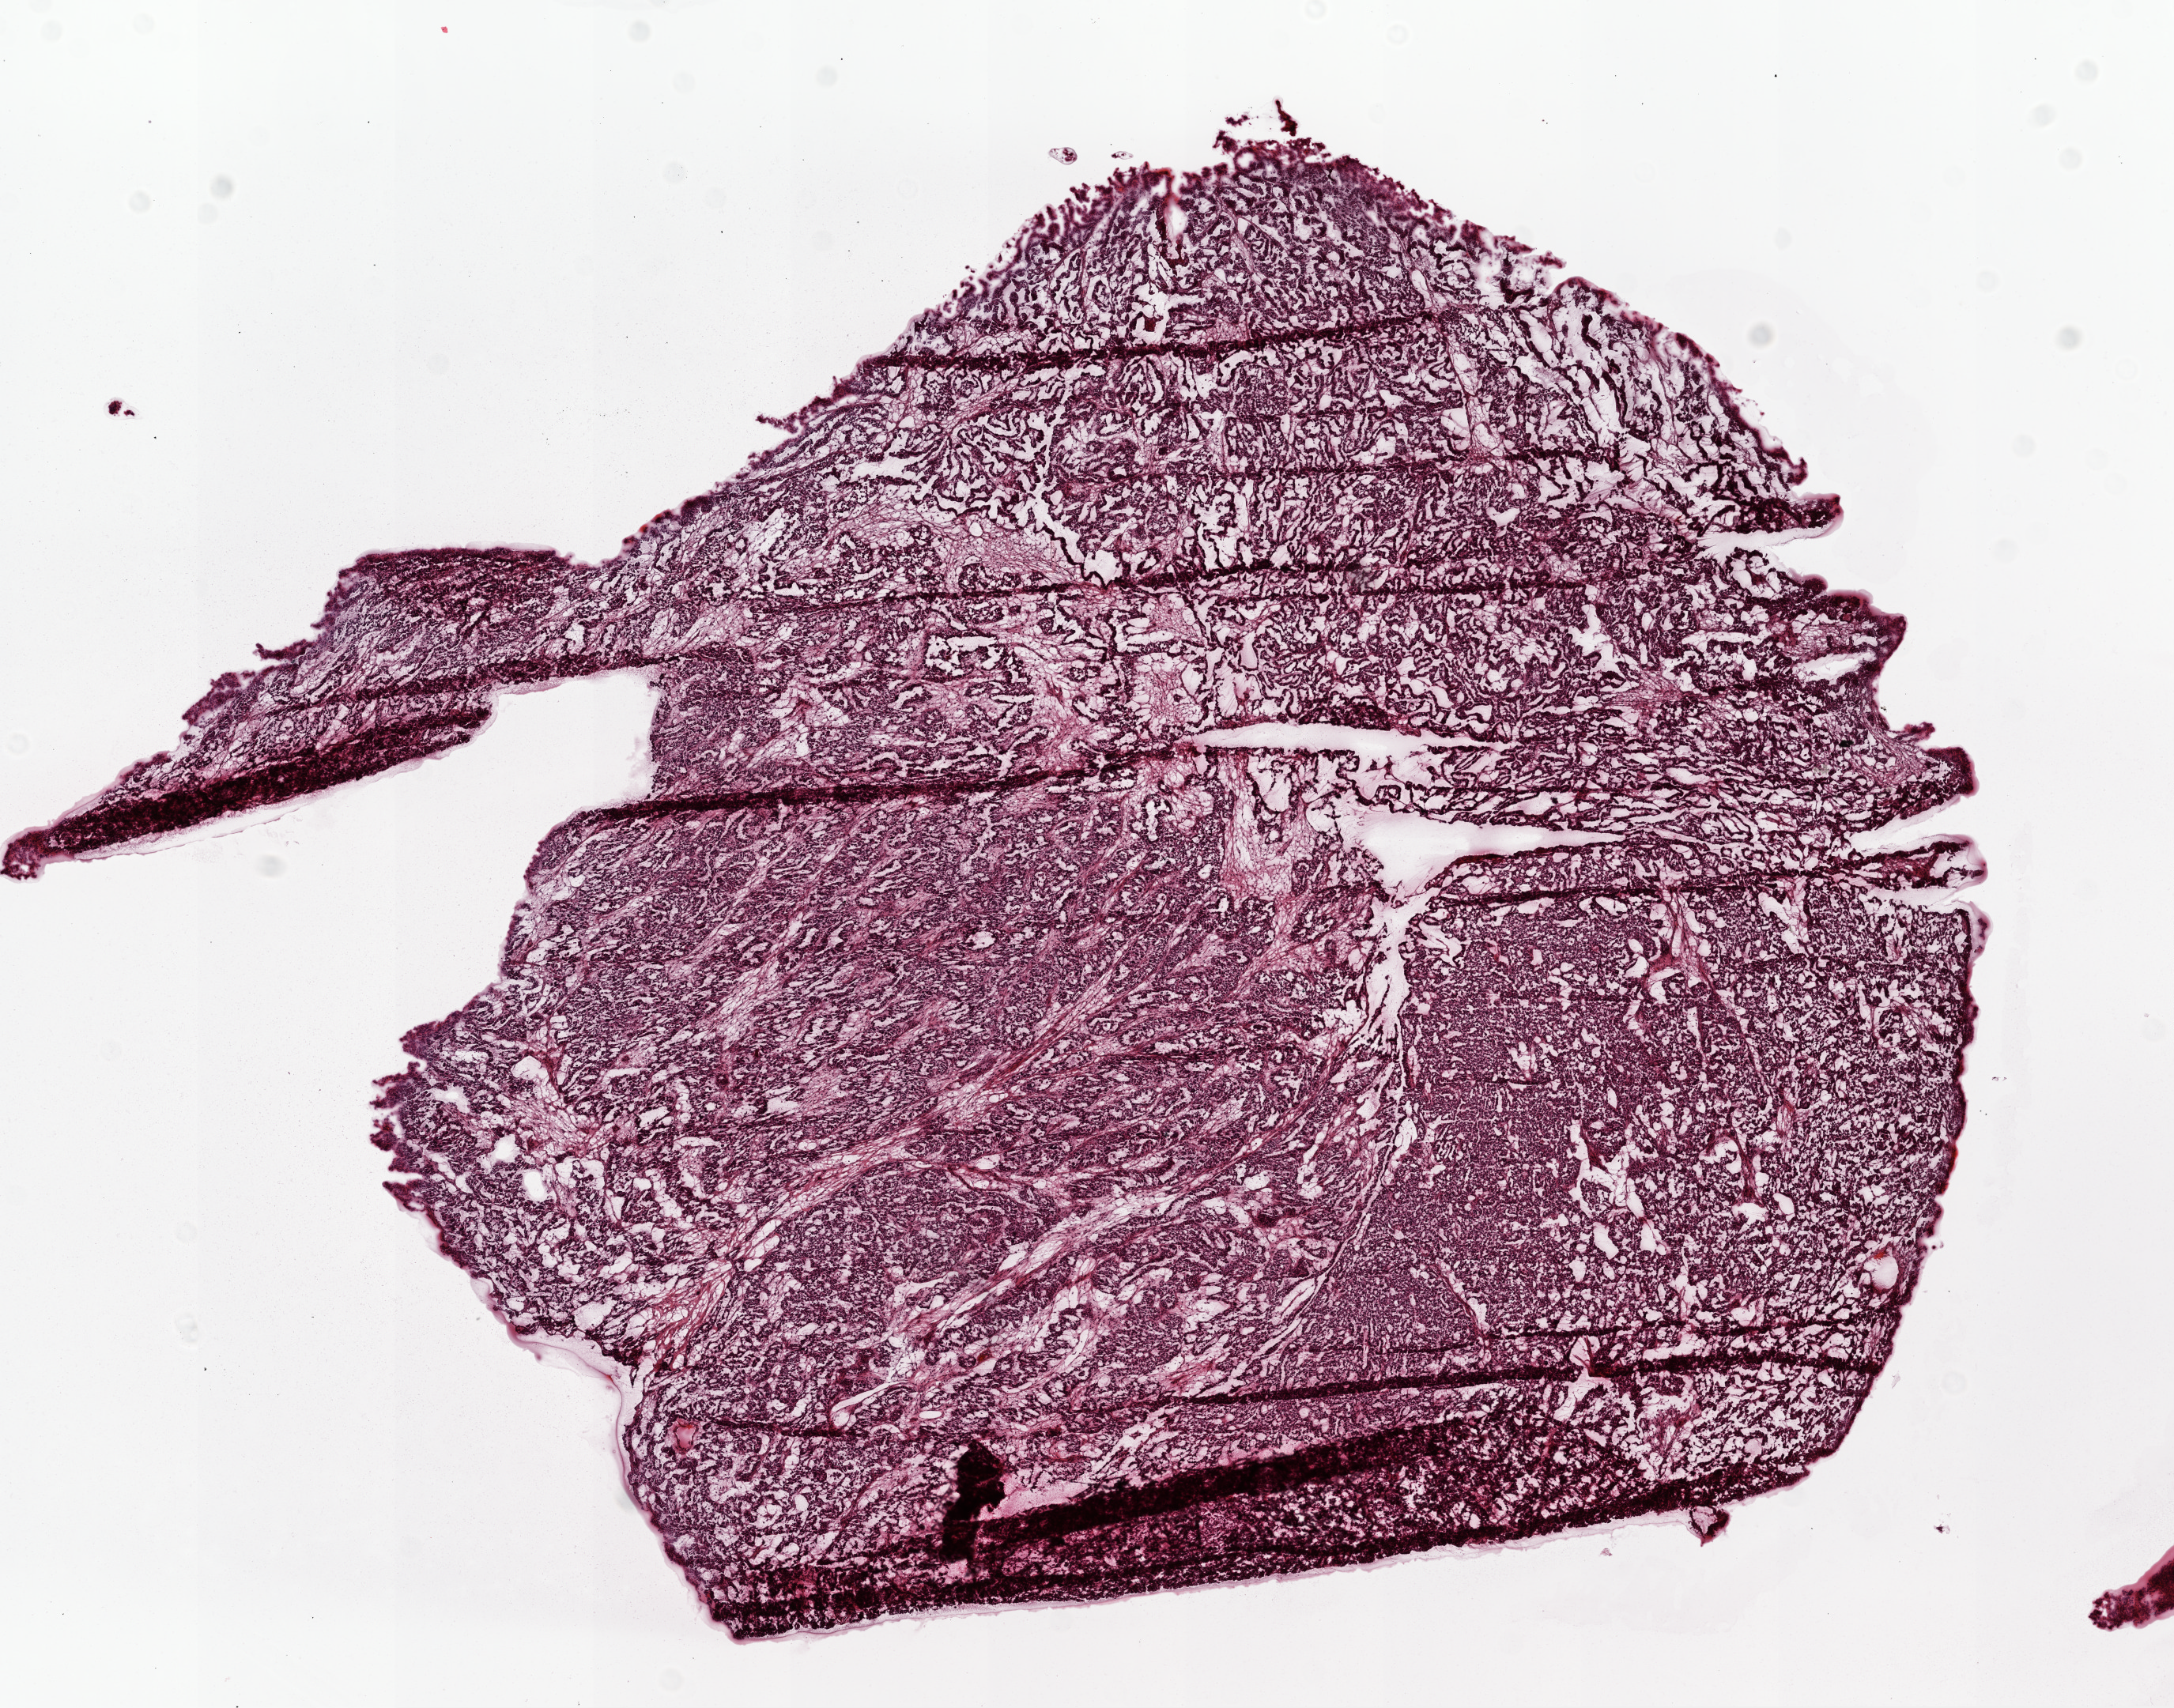
H&E whole-slide image, a low-resolution overview of the entire scanned area, about 11.0 x 8.7 mm (from a 20x scan), frozen section from the top of the tissue portion, primary tumour sample from the ovary. Female patient; age at initial diagnosis 50 years. Histologic grade: G3 (poorly differentiated). Composition of this section per pathologist review: tumour cells 90%, tumour nuclei 80%, normal cells 0%, stromal cells 10%, necrosis 0%. Inflammatory infiltration, as recorded: lymphocyte infiltration 0%, monocyte infiltration 0%, neutrophil infiltration 0%.
- pathologic diagnosis: Serous cystadenocarcinoma, NOS
- FIGO stage: IIIA